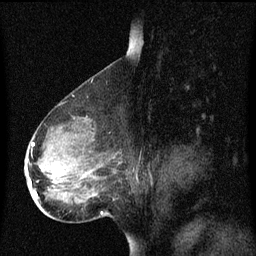
Breast MRI (dynamic contrast-enhanced), one sagittal slice; position 42 of 60 along the scan axis; dynamic contrast-enhanced series, image 2 of 3 at this slice position (ordered by acquisition); 1.5 T; TE 4.2 ms, TR 8.4 ms; 2 mm slice thickness; 256 × 256 image matrix. Patient: female, 49 years. Case-level facts recorded for this patient, not image findings: setting: breast cancer imaged before/during neoadjuvant chemotherapy; receptor status: HR-positive, HER2-negative.
Outlined on this slice (semi-automatic segmentation, software-assisted and operator-edited):
- analysis volume of interest (the breast-tissue region the enhancement analysis was run in; not a lesion): bounding box [x1, y1, x2, y2] px = [26, 126, 121, 201]
- tumour enhancement mask (voxels above the 70 % enhancement threshold inside the analysis volume of interest): [31, 142, 44, 199]